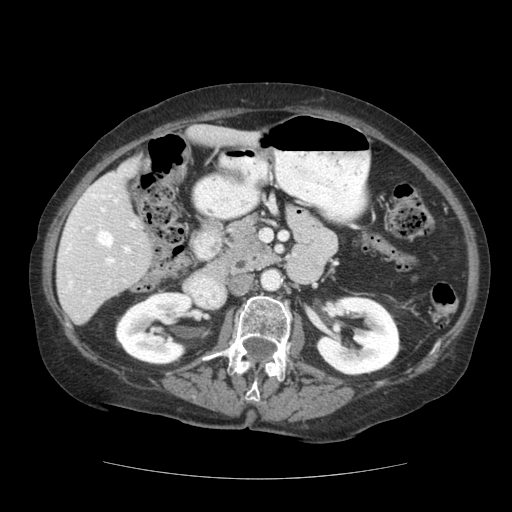
Contrast-enhanced abdominal CT (liver protocol), one axial slice. Slice 58 of 111 in the series (ordered by position). Reconstruction kernel STANDARD. Soft-tissue window (W 400 / L 40 HU). 512 × 512 image matrix, field of view 360 × 360 mm. Case-level facts recorded for this patient, not image findings: diagnosis: hepatocellular carcinoma (patient treated with transarterial chemoembolisation; whether this scan precedes or follows treatment is not stated here); TNM stage (as recorded): Stage-I; Child-Pugh class: A.
Annotated regions visible in this slice (semi-automatic segmentation, software-assisted and operator-edited):
- liver parenchyma outside the tumour (the mass and vessels are separate outlines, so this box may not span the whole liver): bounding box <56,126,260,324> (left, top, right, bottom; pixels)
- liver vessels: <63,182,136,293>